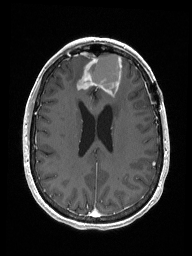
Brain MRI from a brain-tumour surgery series, one axial slice. Slice 66 of 192 in the series (ordered by position). T1-weighted post-contrast. 192 × 256 image matrix, field of view 187 × 250 mm. Case-level facts recorded for this patient, not image findings: histopathology: Metastastic Carcinoma from Breast primary; tumour location: Right Frontal.
Structures marked on this image (outlined manually by an expert reader):
- previous resection cavity: bounding box <88,53,122,96> (left, top, right, bottom; pixels)